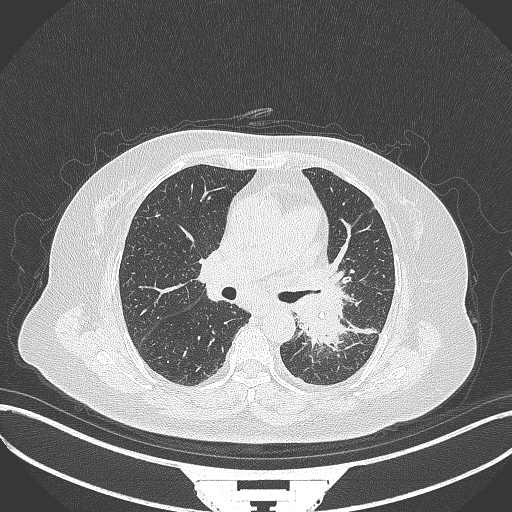
Chest CT, one axial slice. Reconstruction kernel B70f. Lung window (W 1500 / L -600 HU). 1 mm slice thickness. 512 × 512 image matrix, field of view 400 × 400 mm. Patient: female, 69 years. From the clinical record (not read from this slice): clinical TNM (as recorded): T2b N3 M1.
Outlined on this slice (rectangle marked by the reading radiologist):
- lung tumour (recorded histology: adenocarcinoma): box from (x=289, y=282) to (x=349, y=357) px